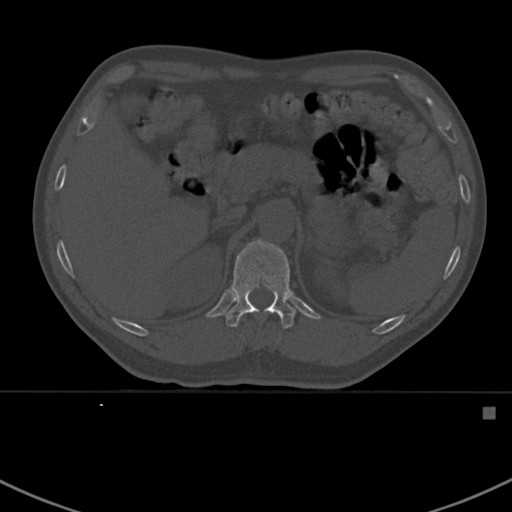
CT including the spine, one axial slice. Slice 332 of 412 in the series (ordered by position). Reconstruction kernel Br40s. 120 kVp. Bone window (W 1800 / L 400 HU). 1.5 mm slice thickness. 512 × 512 image matrix, field of view 358 × 358 mm. Male patient, age 59 years. From the clinical record (not read from this slice): primary cancer: prostate.
Outlined on this slice (semi-automatic segmentation, software-assisted and operator-edited):
- T12 vertebra: box from (x=225, y=238) to (x=296, y=329) px